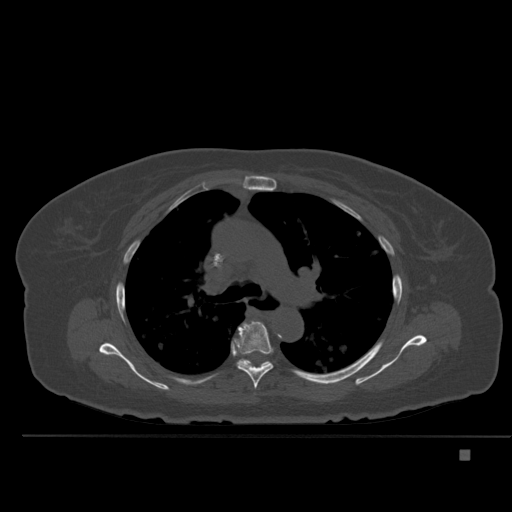
CT including the spine, one axial slice. Position 351 of 477 along the scan axis. Bone window (W 1800 / L 400 HU). 1.5 mm slice thickness. 512 × 512 image matrix. Patient: female, 74 years. From the clinical record (not read from this slice): primary cancer: colon.
Outlined on this slice (semi-automatically segmented with operator editing):
- T5 vertebra: box from (x=234, y=320) to (x=273, y=389) px
- T6 vertebra: (x=233, y=341)–(x=272, y=368)